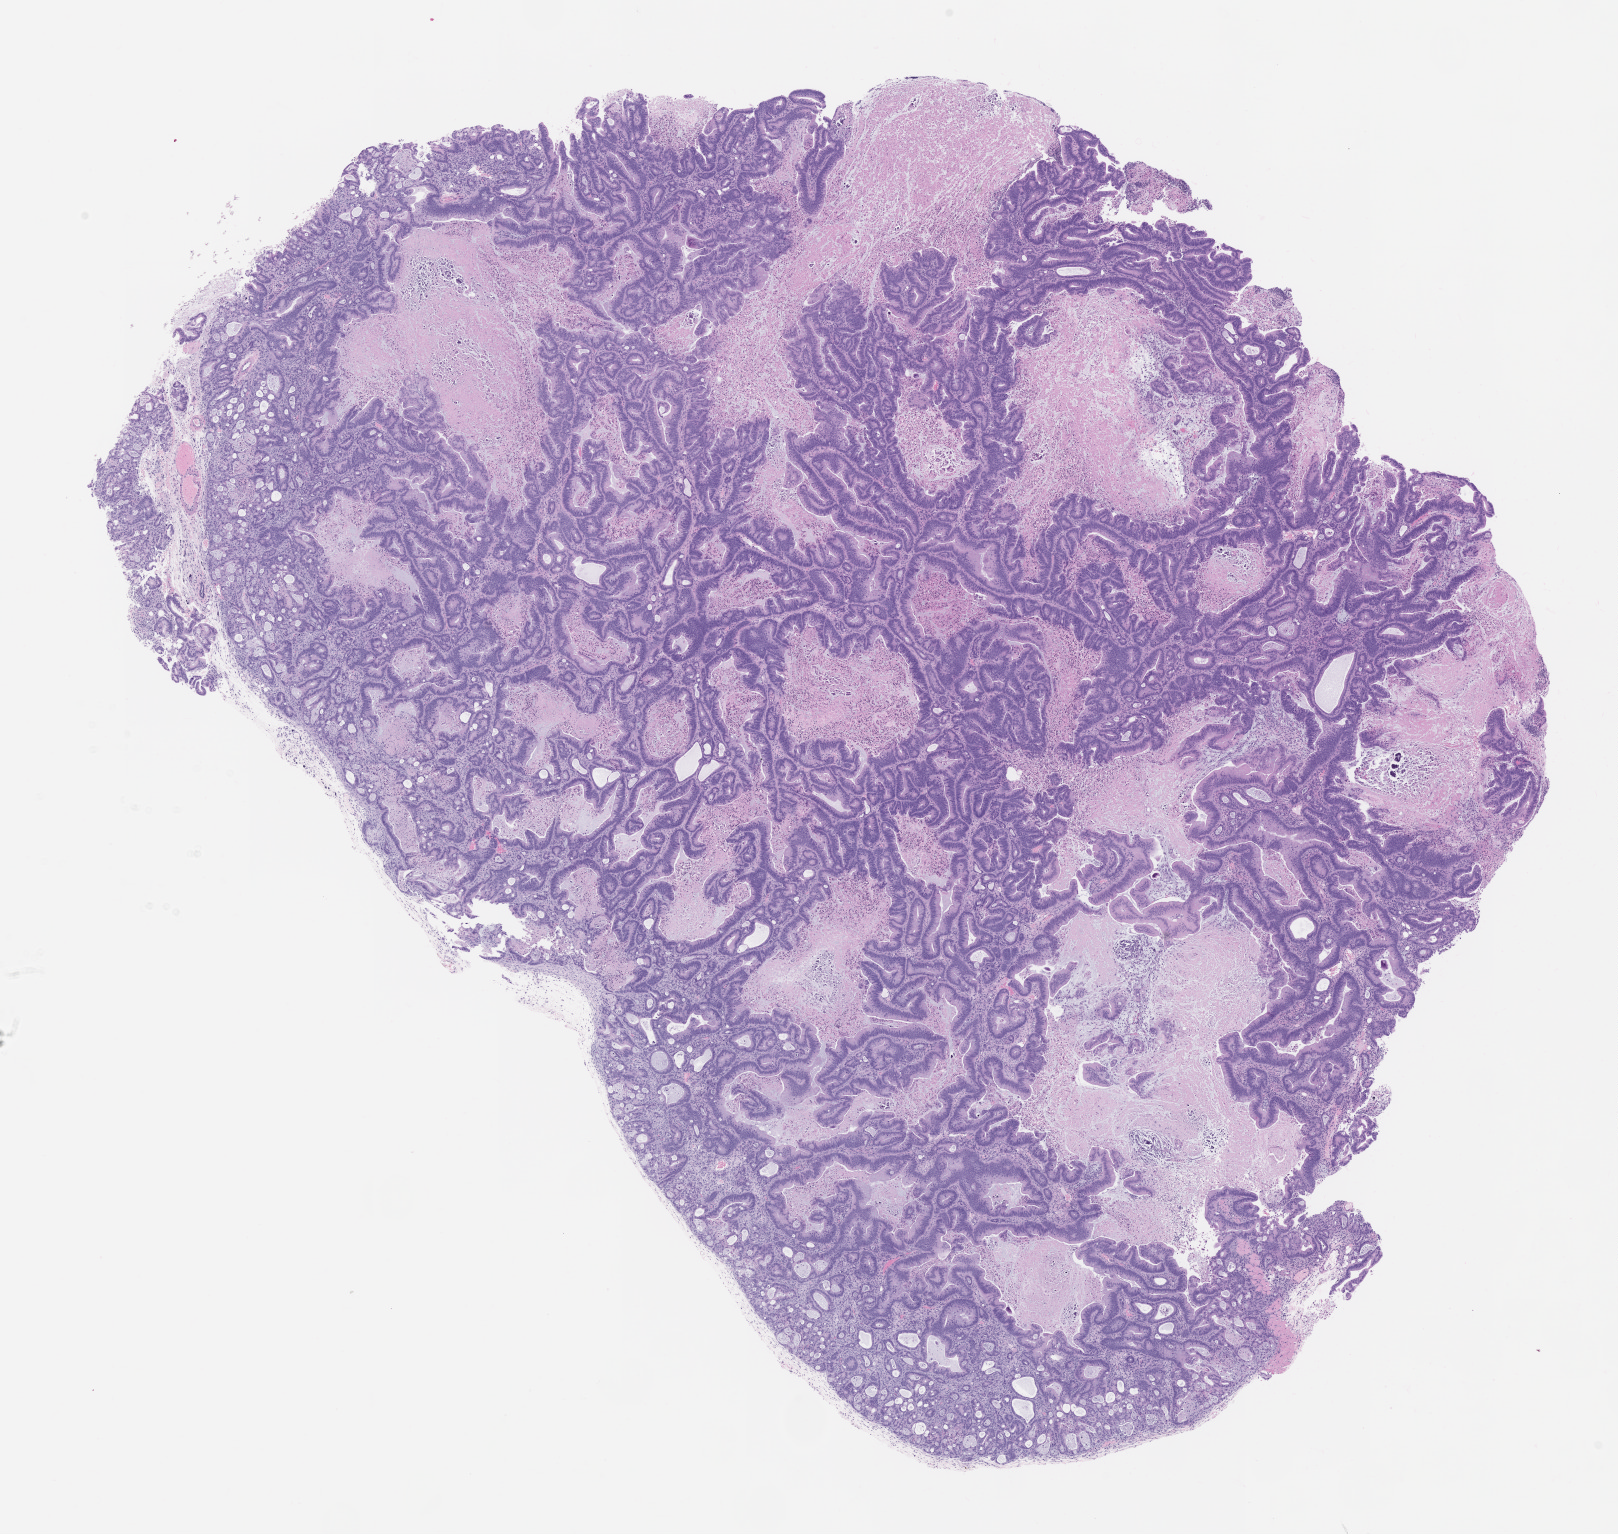
Hematoxylin and eosin (H&E) whole-slide image of a patient-derived xenograft (PDX) tumor grown in a mouse, passage 1, whole scanned area (about 13.0 x 12.3 mm) shown as a low-resolution overview, formalin-fixed paraffin-embedded section, tumor site category: colon.
Originating patient diagnosis: Colon Adenocarcinoma.